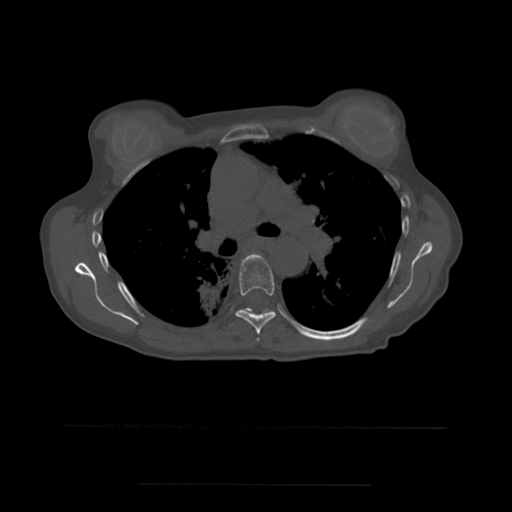
CT including the spine, one axial slice. Slice 375 of 544 in the series (ordered by position). Bone window (W 1800 / L 400 HU). 1.25 mm slice thickness. 512 × 512 image matrix, field of view 350 × 350 mm. Patient age 58 years. Case-level facts recorded for this patient, not image findings: primary cancer: lung.
Structures marked on this image (semi-automatically segmented with operator editing):
- T5 vertebra: box from (x=252, y=253) to (x=259, y=340) px
- T6 vertebra: (x=236, y=254)–(x=276, y=335)
- T7 vertebra: (x=241, y=309)–(x=246, y=311)